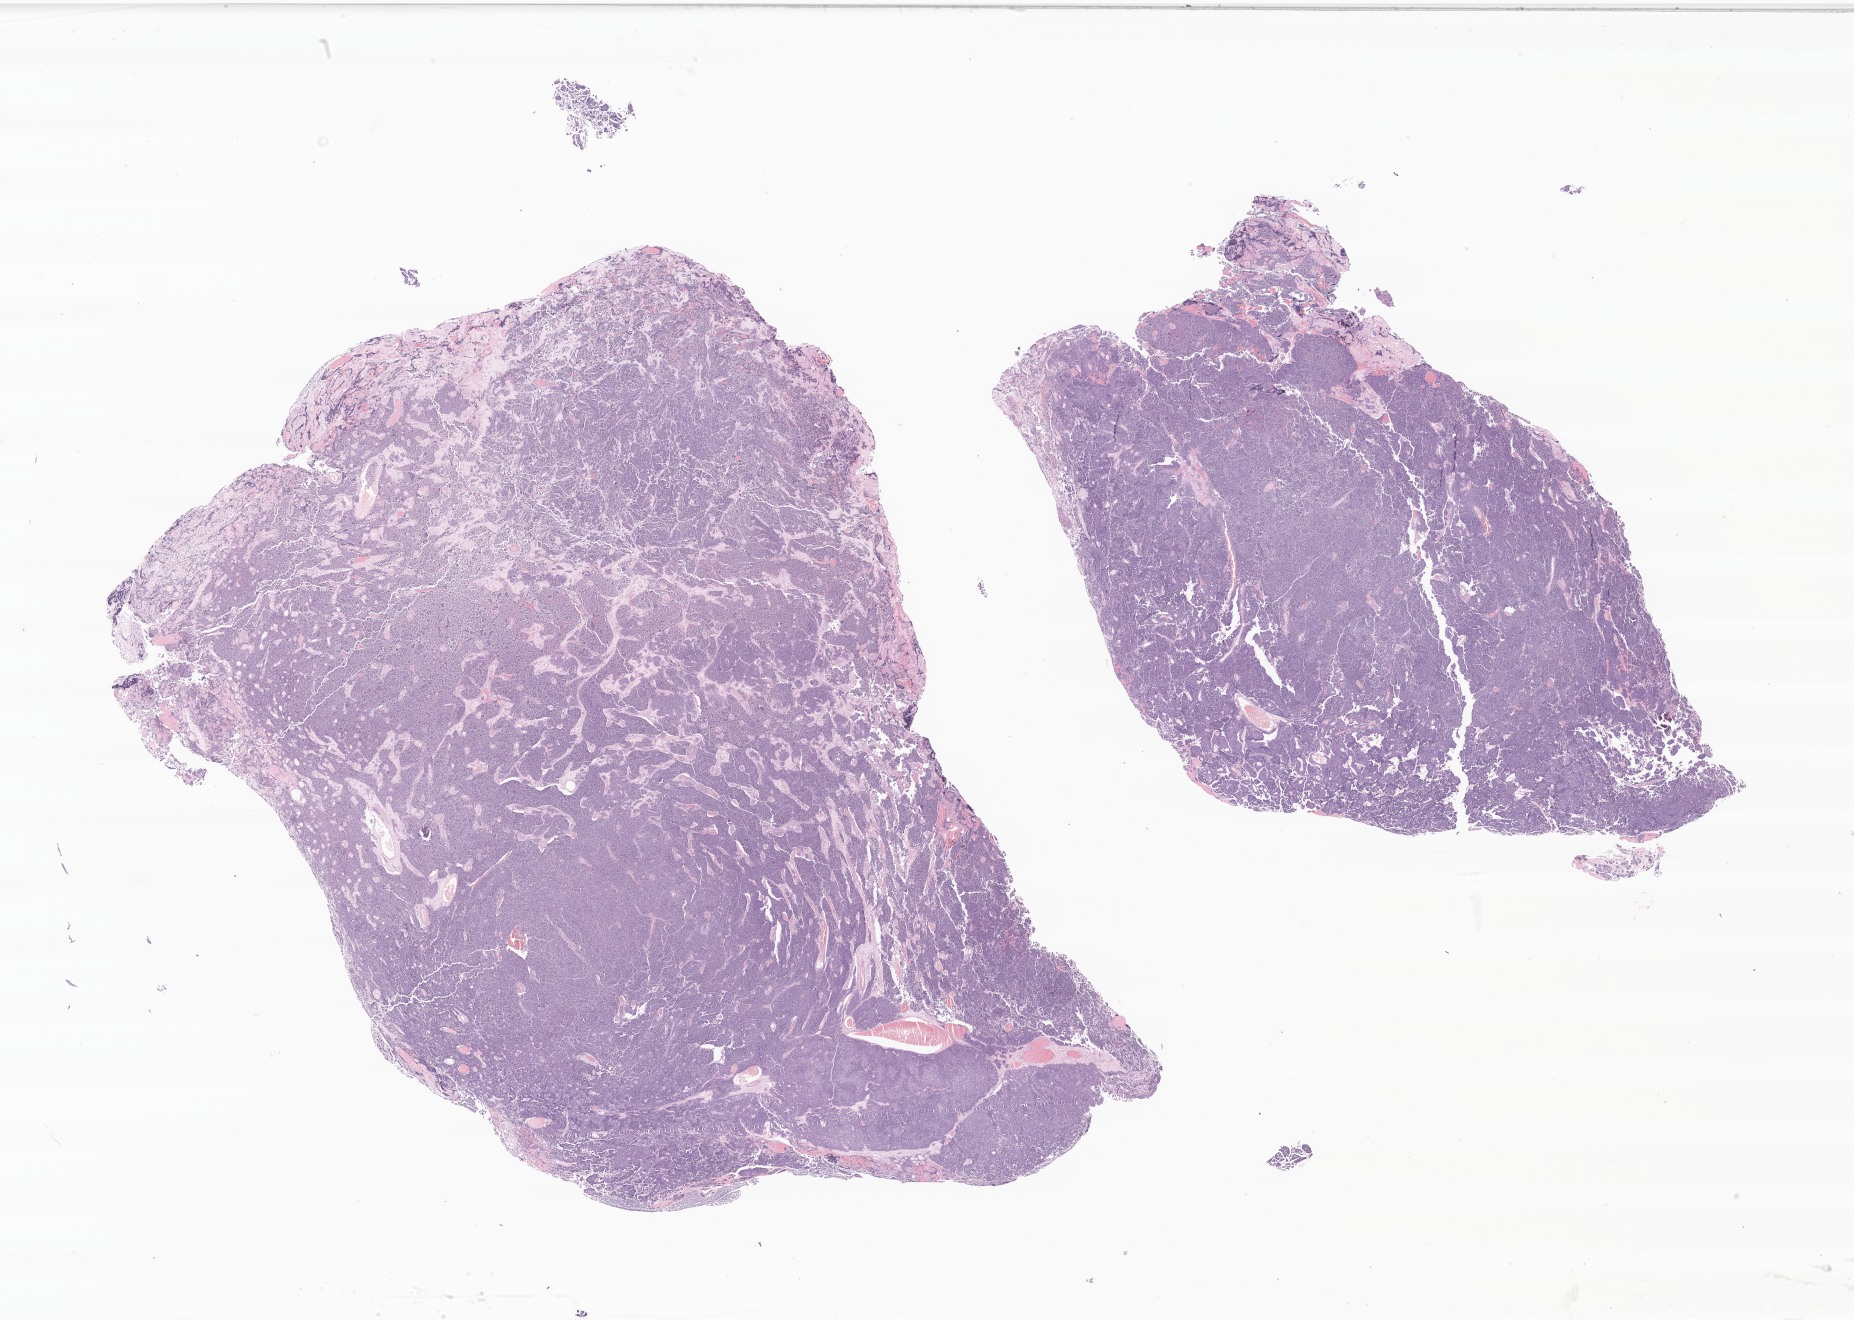
Whole-slide image, H&E stain of tumor tissue from the brain stem, a low-resolution overview of the entire scanned area, about 31.3 x 22.3 mm; FFPE section. Female patient, age 848 days.
Recorded diagnosis: Medulloblastoma, NOS.